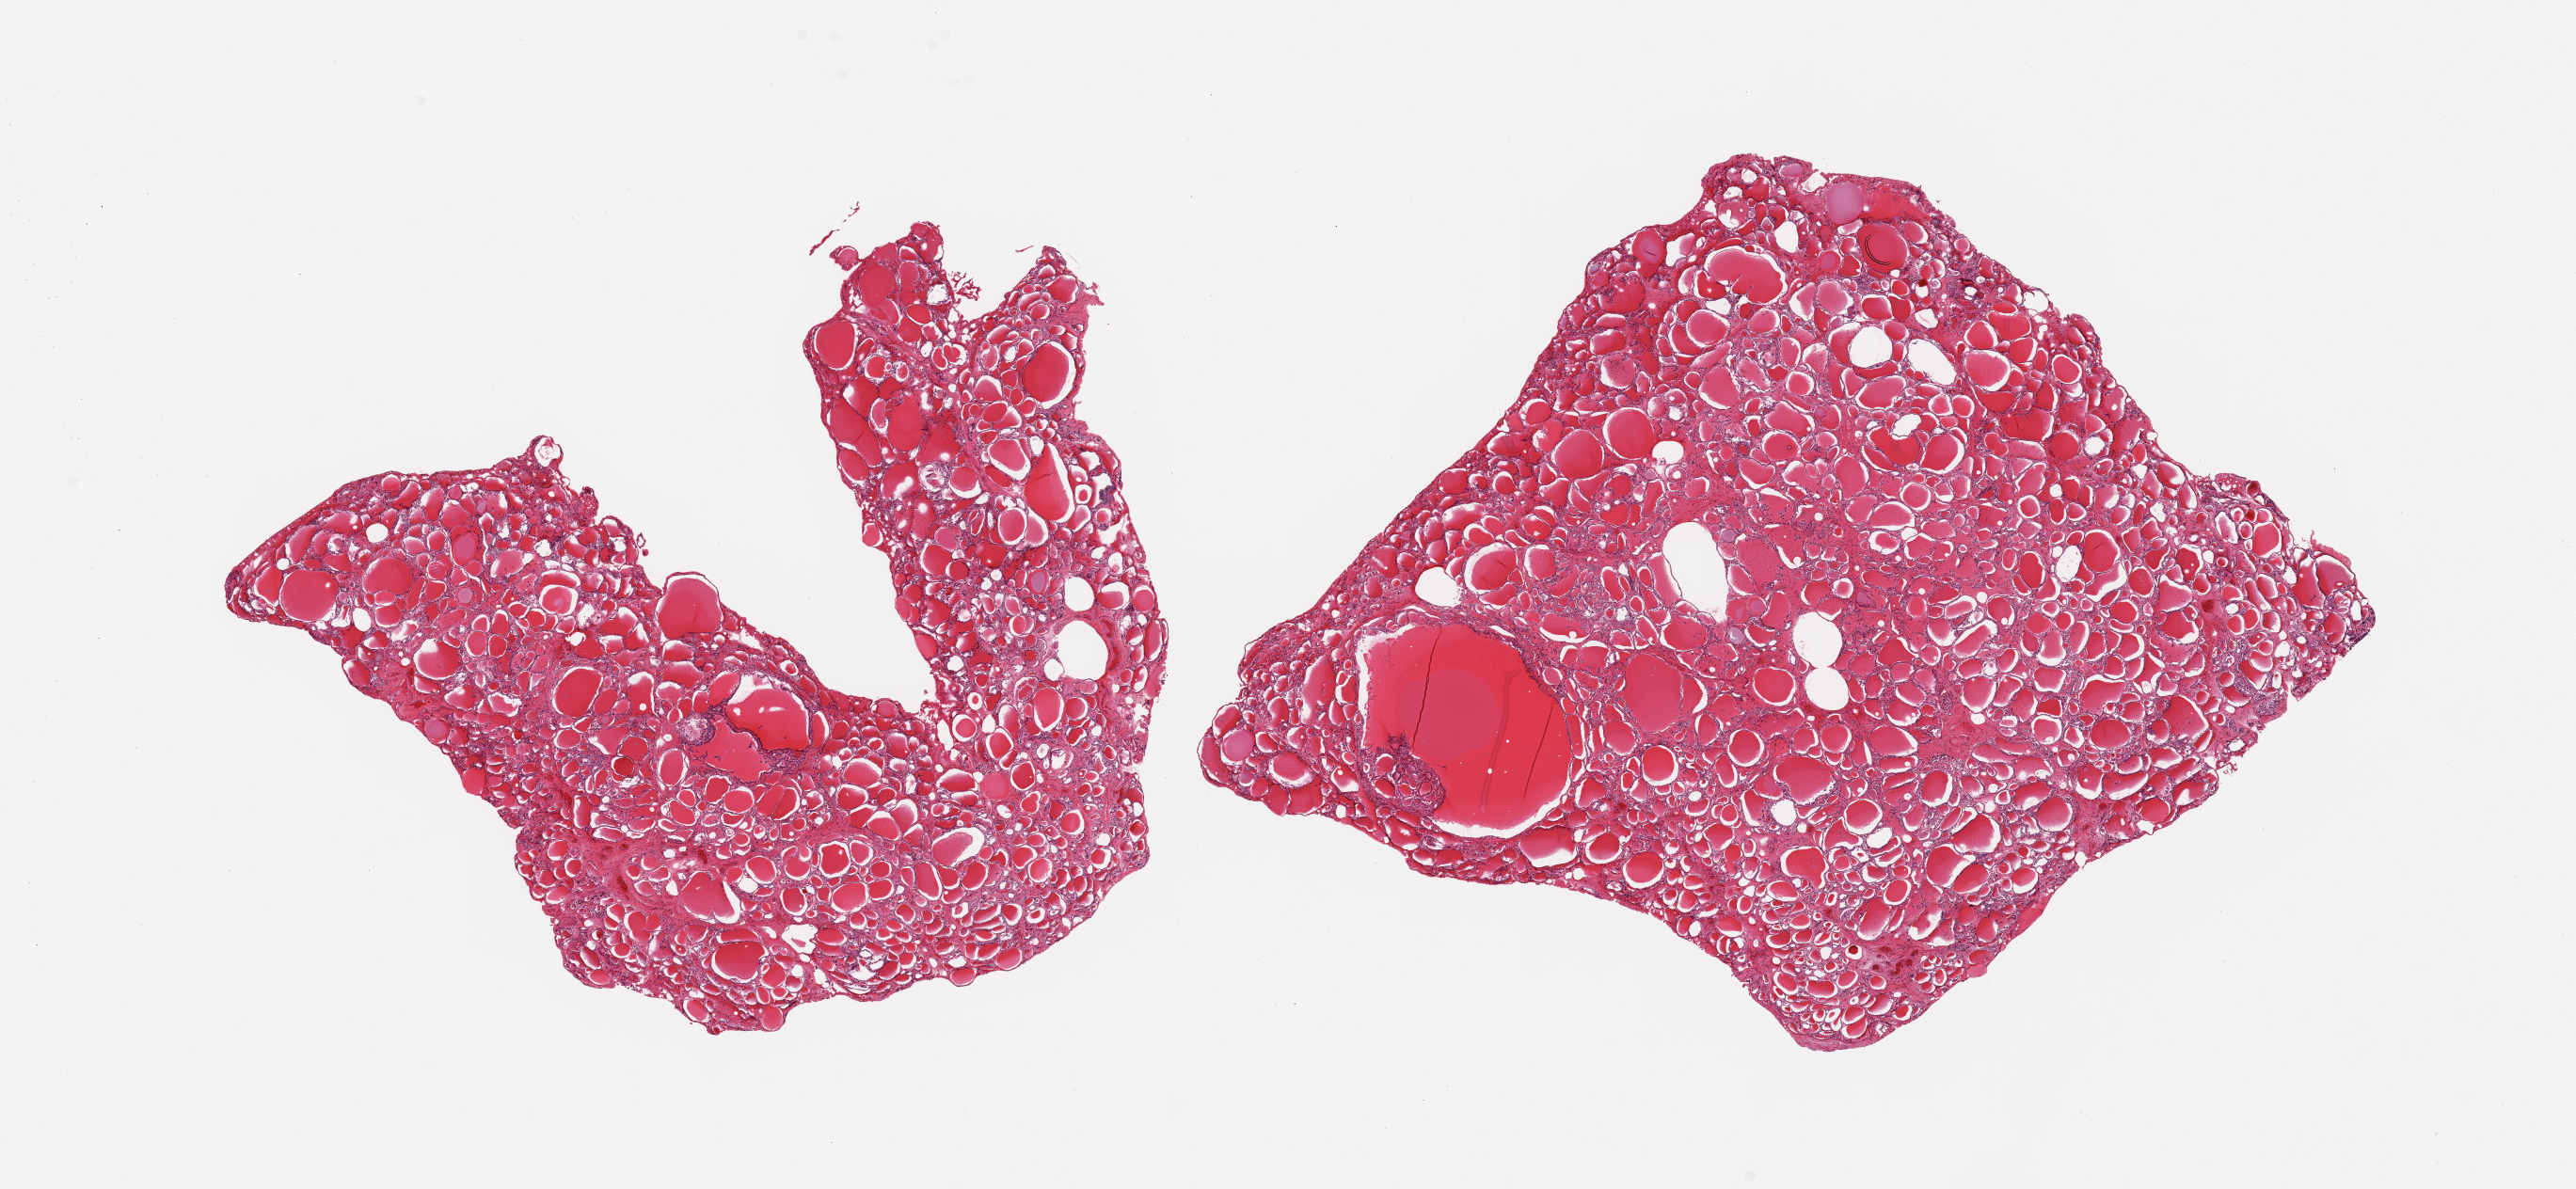
Digitized haematoxylin and eosin-stained section, shown as a low-resolution overview of the whole scanned area (about 21.7 x 10.0 mm). PAXgene-fixed paraffin-embedded (PFPE) section. Section of thyroid (target tissue). Tissue donor sample. Donor sex: male.
Reviewer comment on this tissue sample: 2 pieces.